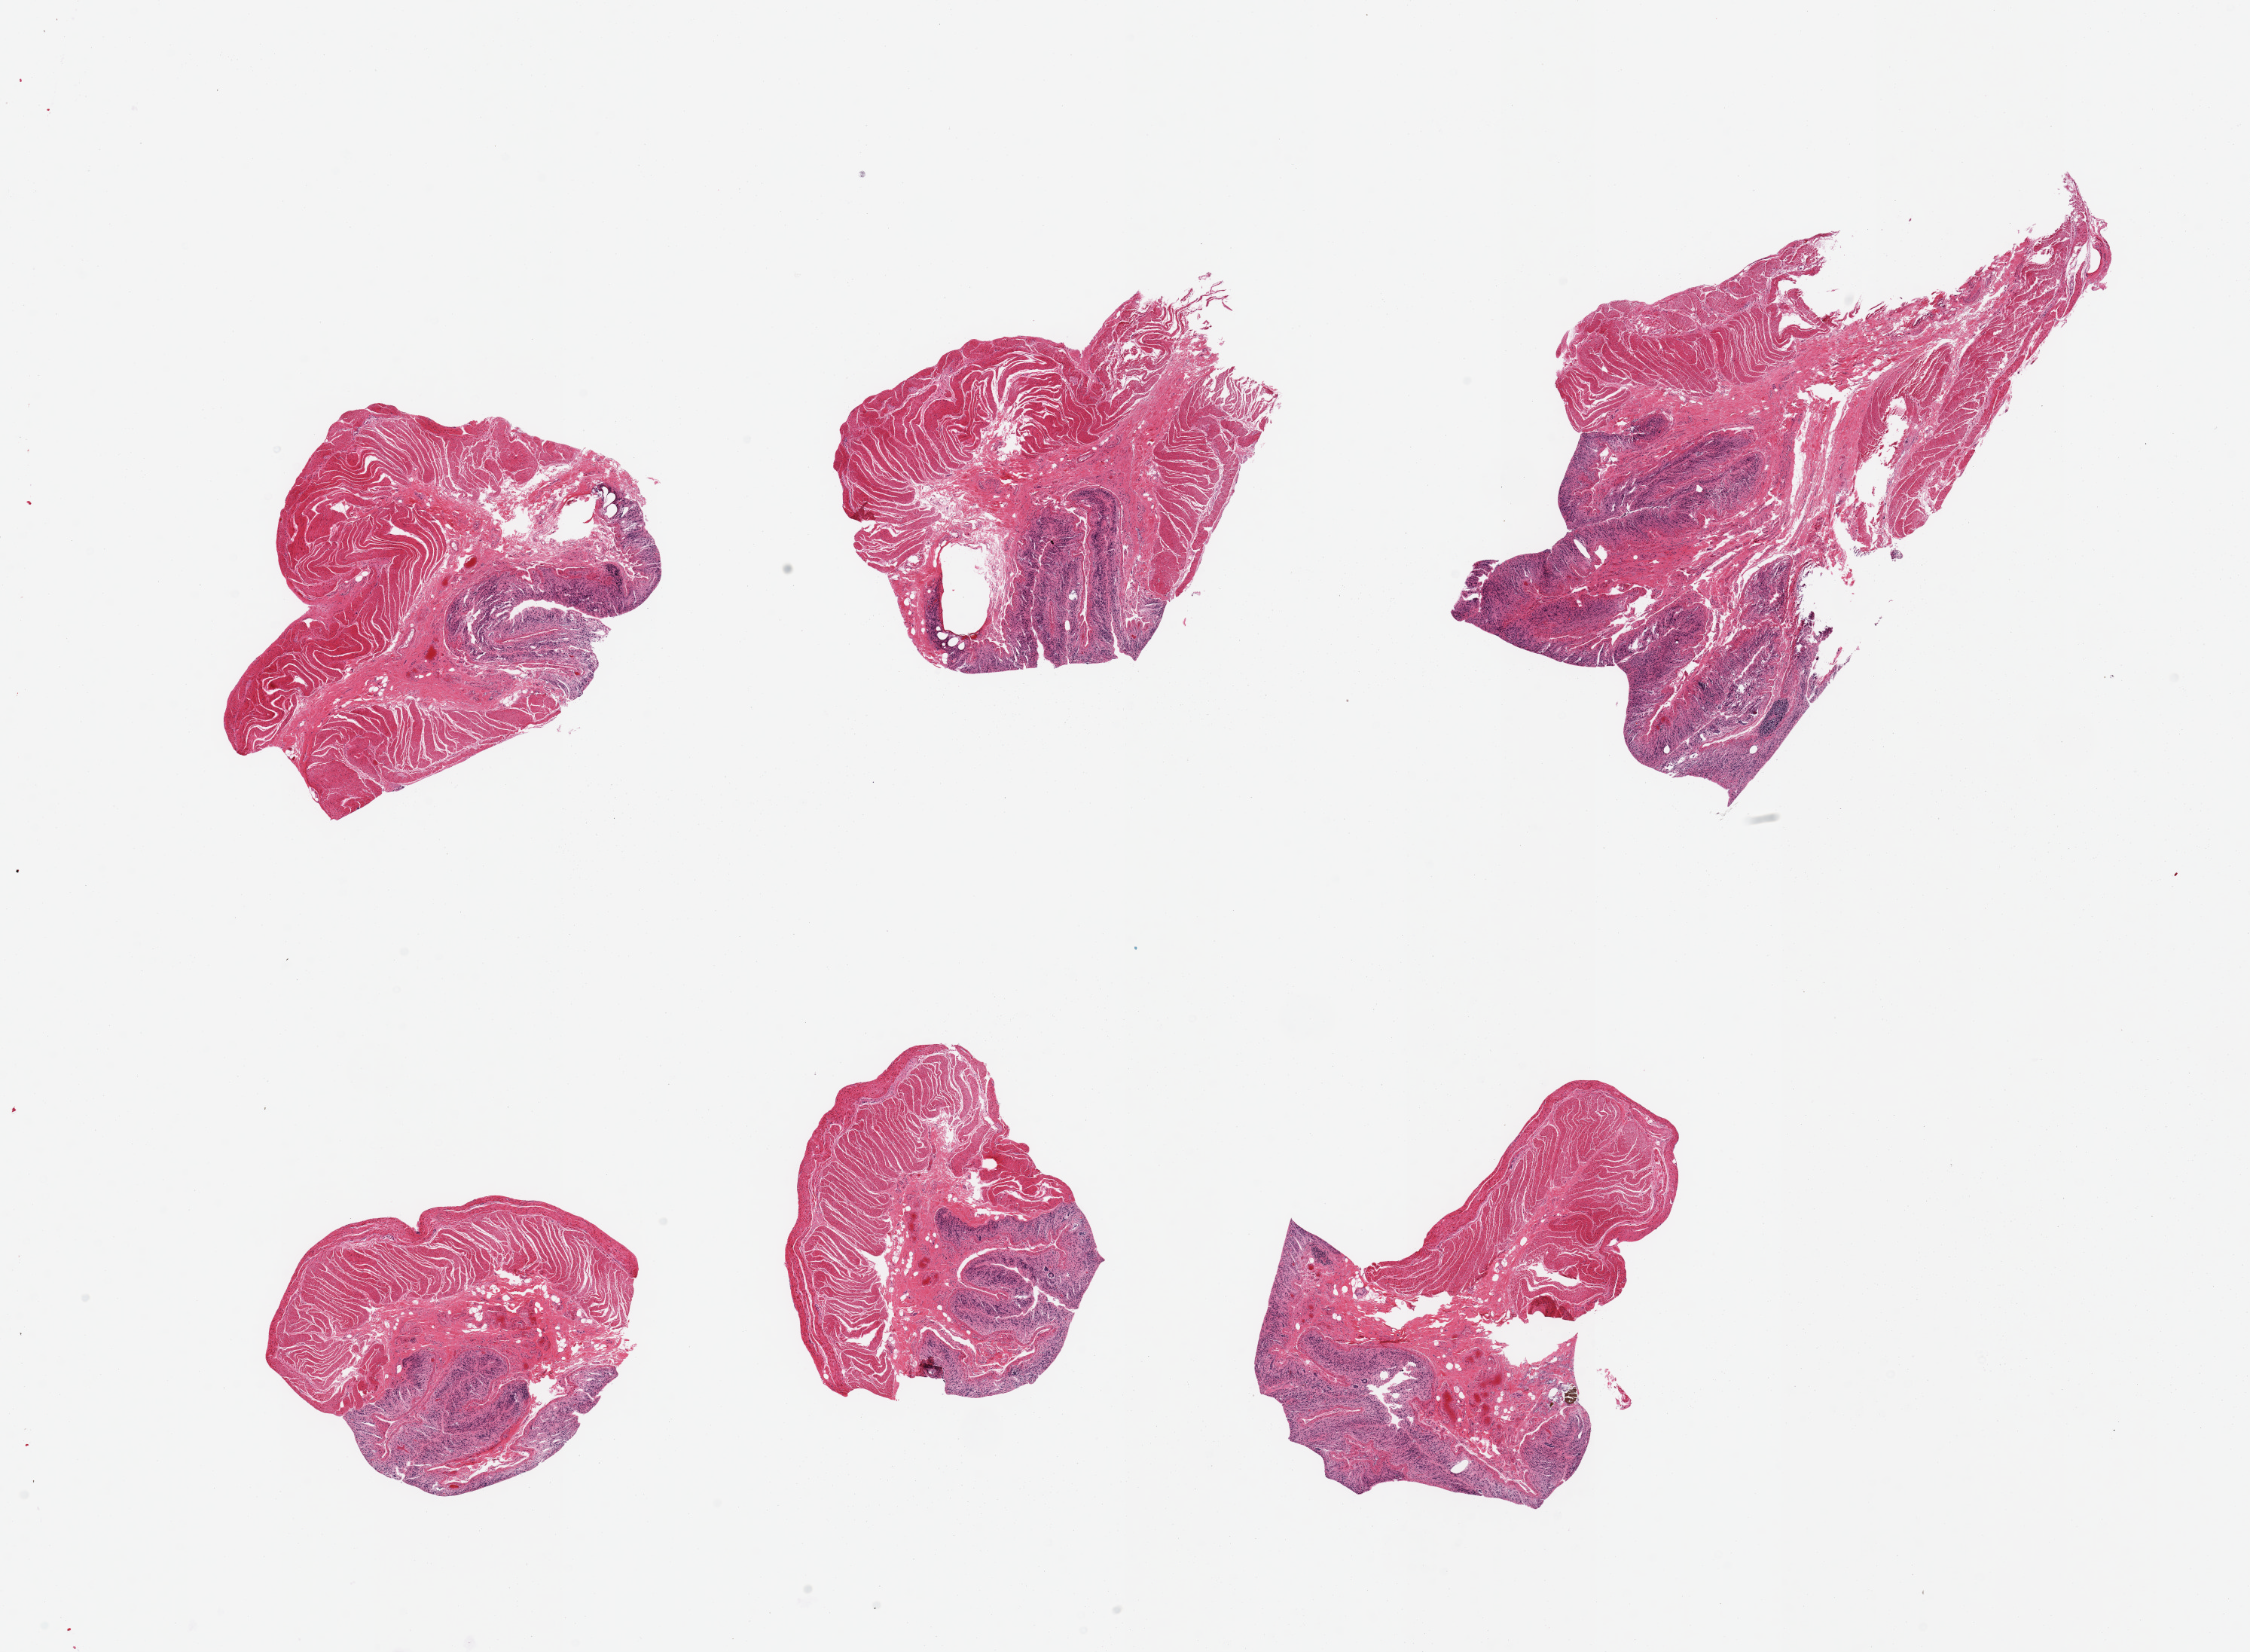
Hematoxylin and eosin (H&E) whole-slide image, low-resolution overview of the scanned area, about 23.6 x 17.3 mm (acquisition: 20x scan), PAXgene-fixed paraffin-embedded (PFPE) section, target tissue: transverse colon, donor tissue sample.
Pathologist's review note for this sample: 6 pieces, target mucosa up to ~0.25mm, advanced autolysis, glandular elements sloughed, lamina propria remnants present.